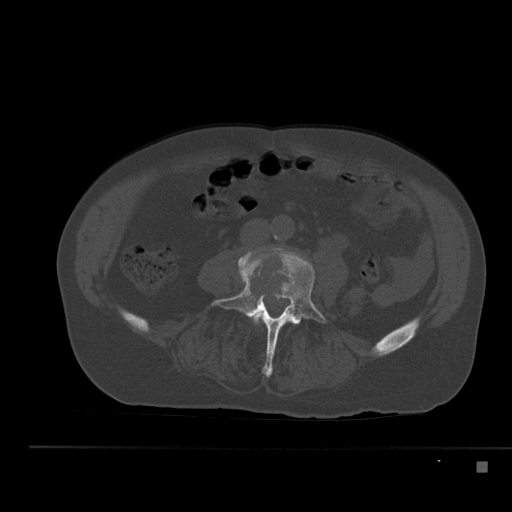
CT including the spine, one axial slice; slice 145 of 517 in the series (ordered by position); reconstruction kernel Br40s; 120 kVp; bone window (W 1800 / L 400 HU); 512 × 512 image matrix. Patient: male, 70 years. From the clinical record (not read from this slice): primary cancer: renal; vertebrae with lytic lesions (as recorded): T4, T6, T10, T12, L3, L4, L5.
Structures marked on this image (semi-automatic segmentation, software-assisted and operator-edited):
- L3 vertebra: bounding box (x1, y1, x2, y2) in pixels: (252, 311, 277, 342)
- L4 vertebra: (211, 253, 328, 377)